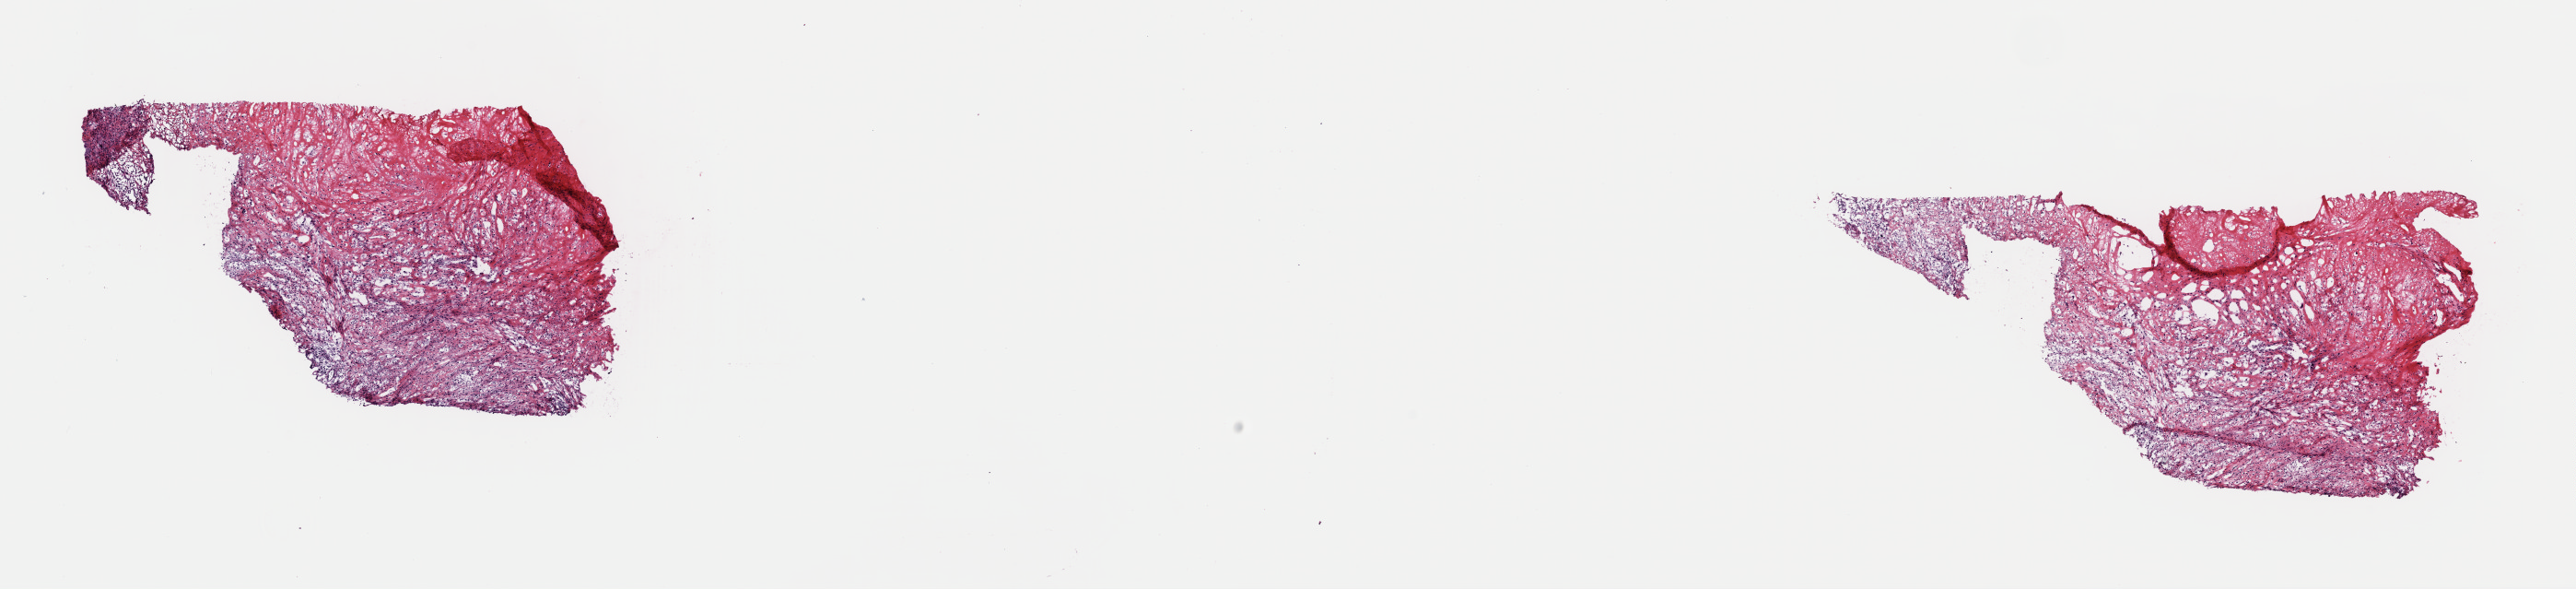
Digitized H&E-stained tissue section (whole slide), whole scanned area (about 22.1 x 5.0 mm) shown as a low-resolution overview. Frozen section from the top of the tissue portion. Sample: primary tumour, connective, subcutaneous and other soft tissues. Male patient; age at initial diagnosis 29 years. Pathologist review of this section (percent, as recorded): tumour cells 96%, tumour nuclei 75%, normal cells 0%, stromal cells 0%, necrosis 4%. Infiltration values recorded for this section: lymphocyte infiltration 1%, monocyte infiltration 0%, neutrophil infiltration 0%.
- histologic diagnosis: Malignant peripheral nerve sheath tumor